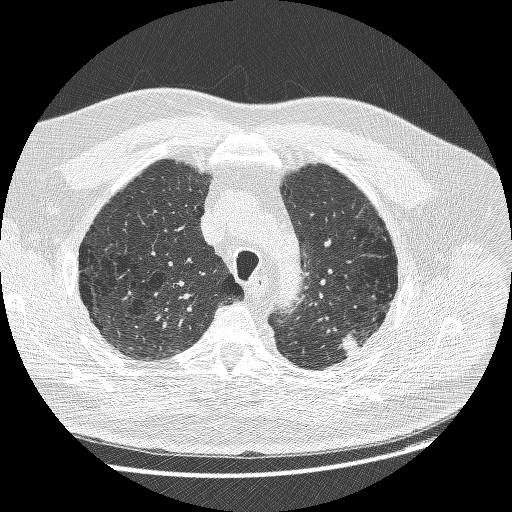
Chest CT (low-dose screening protocol), one axial image, baseline annual screen, lung window (W 1500 / L -600 HU), 1.25 mm slice thickness, lung (sharp) reconstruction kernel (BONE), 120 kVp, slice 206 of 258 in the series. Male participant, aged 68 years at enrolment.
- Expert-annotated lung lesion, bounding box (x1, y1, x2, y2) in pixels: (330, 323, 388, 365).
- Screening reader's record for this exam (one nodule recorded; not confirmed to be the boxed lesion): non-calcified nodule or mass ≥4 mm, left upper lobe, 15 × 14 mm, smooth margins, soft tissue attenuation.
- Later outcome: lung cancer diagnosed 19 days after this screen — adenosquamous carcinoma, left upper lobe, poorly differentiated (G3), stage IIIB (AJCC 6th edition), 32 mm at pathology.